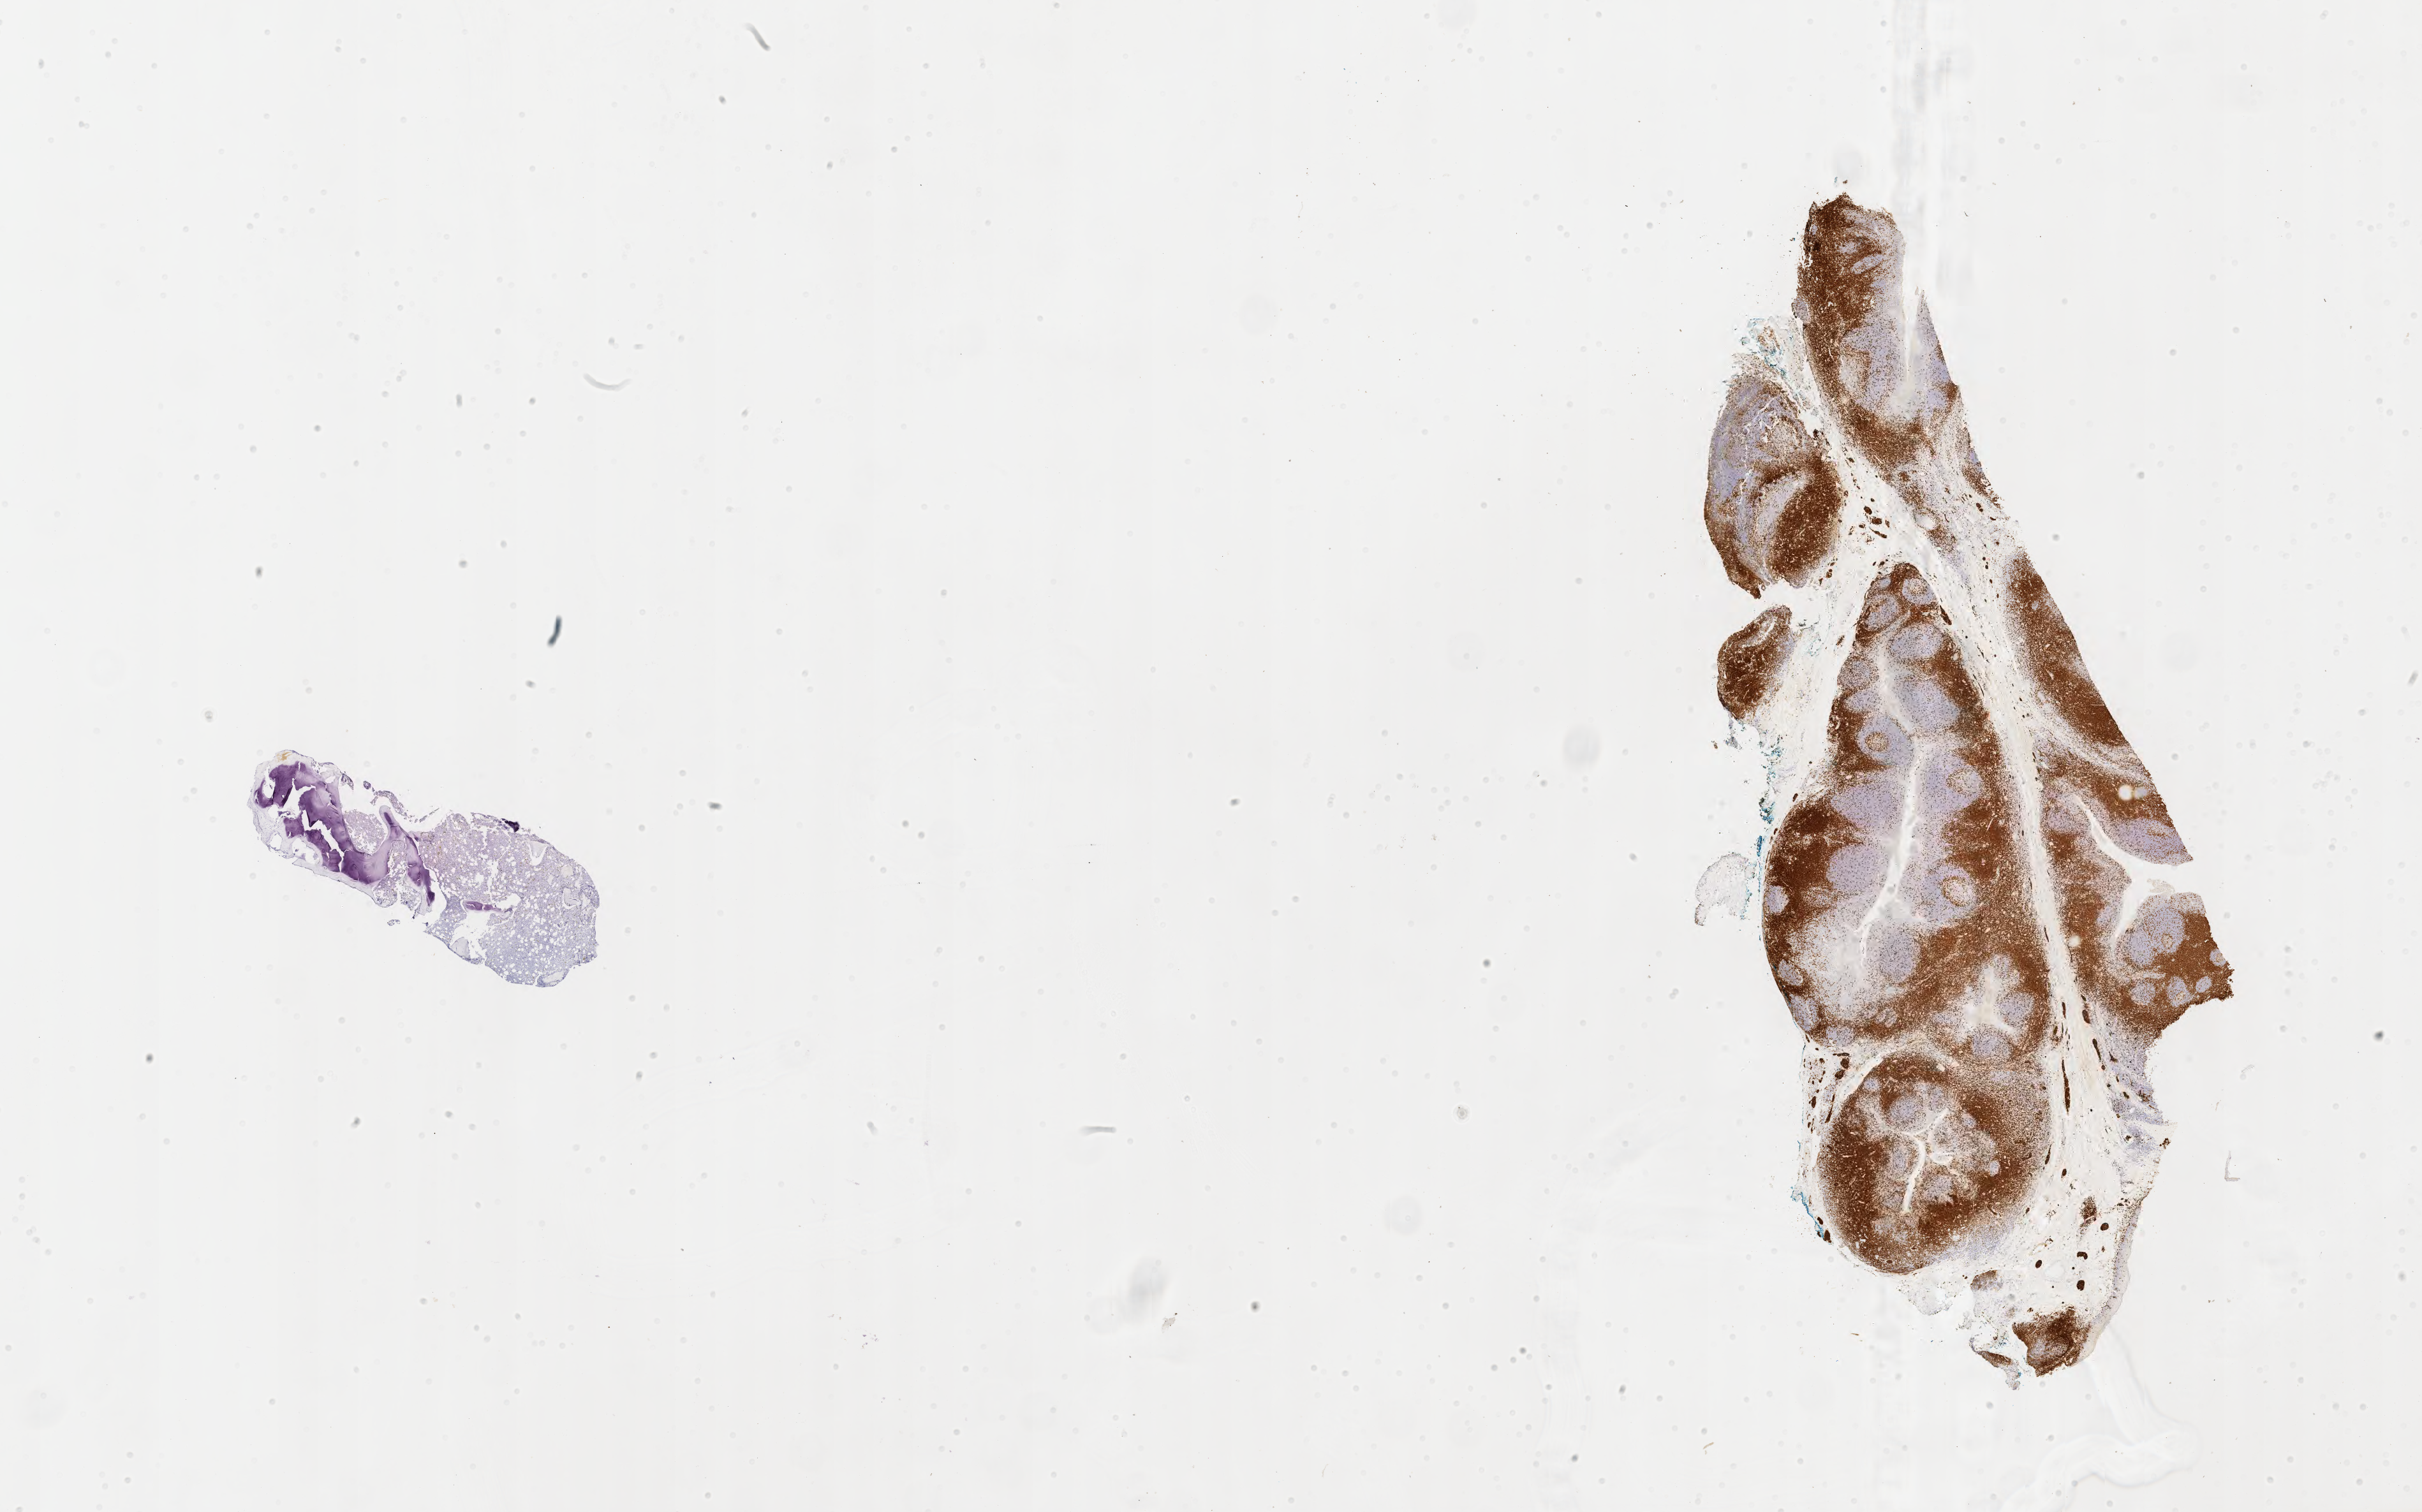
Immunohistochemistry (IHC) whole-slide image stained for CD3, shown as a low-resolution overview of the whole scanned area (about 30.7 x 19.2 mm), tumor tissue, site: bone marrow. Patient: male, 15 years old.
• diagnosis: Burkitt lymphoma, NOS